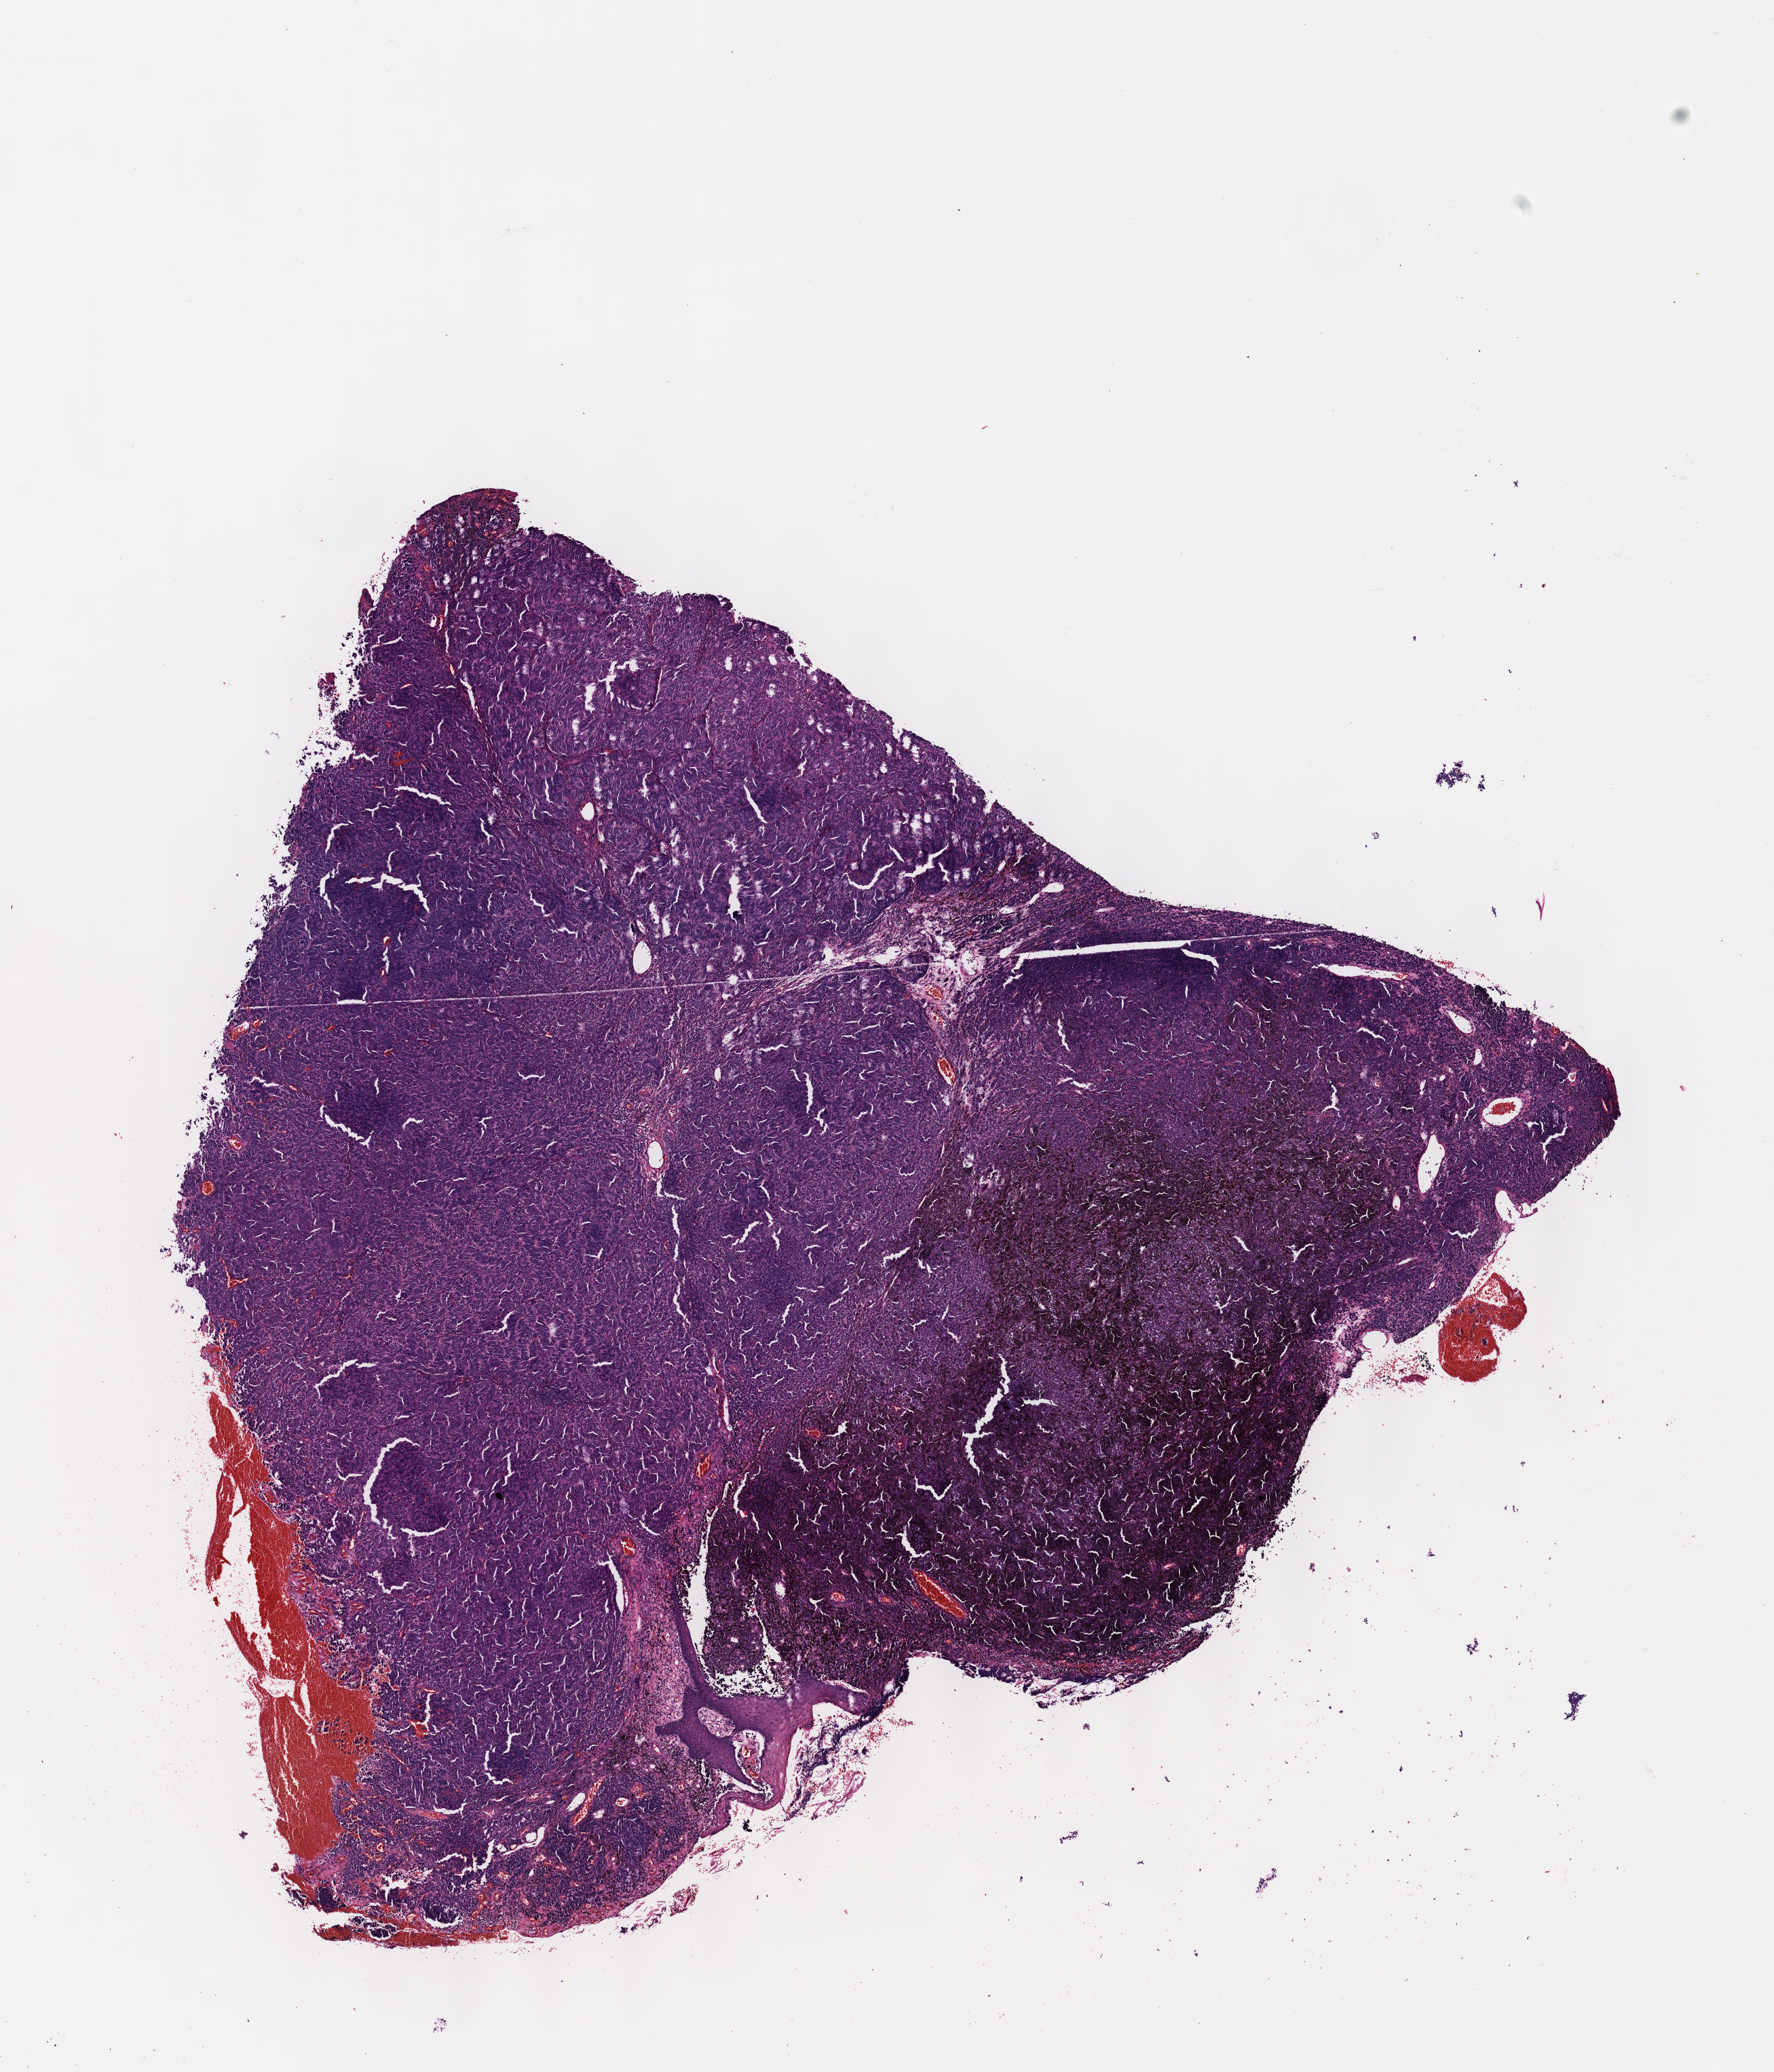
Hematoxylin and eosin (H&E) stained whole-slide image — whole scanned area (about 10.6 x 12.3 mm) shown as a low-resolution overview. Formalin-fixed paraffin-embedded (FFPE) diagnostic section. Sample: primary tumour, skin. Female patient; age at initial diagnosis 71 years.
AJCC pathologic stage: IIB (7th edition). Pathologic diagnosis: Malignant melanoma, NOS.